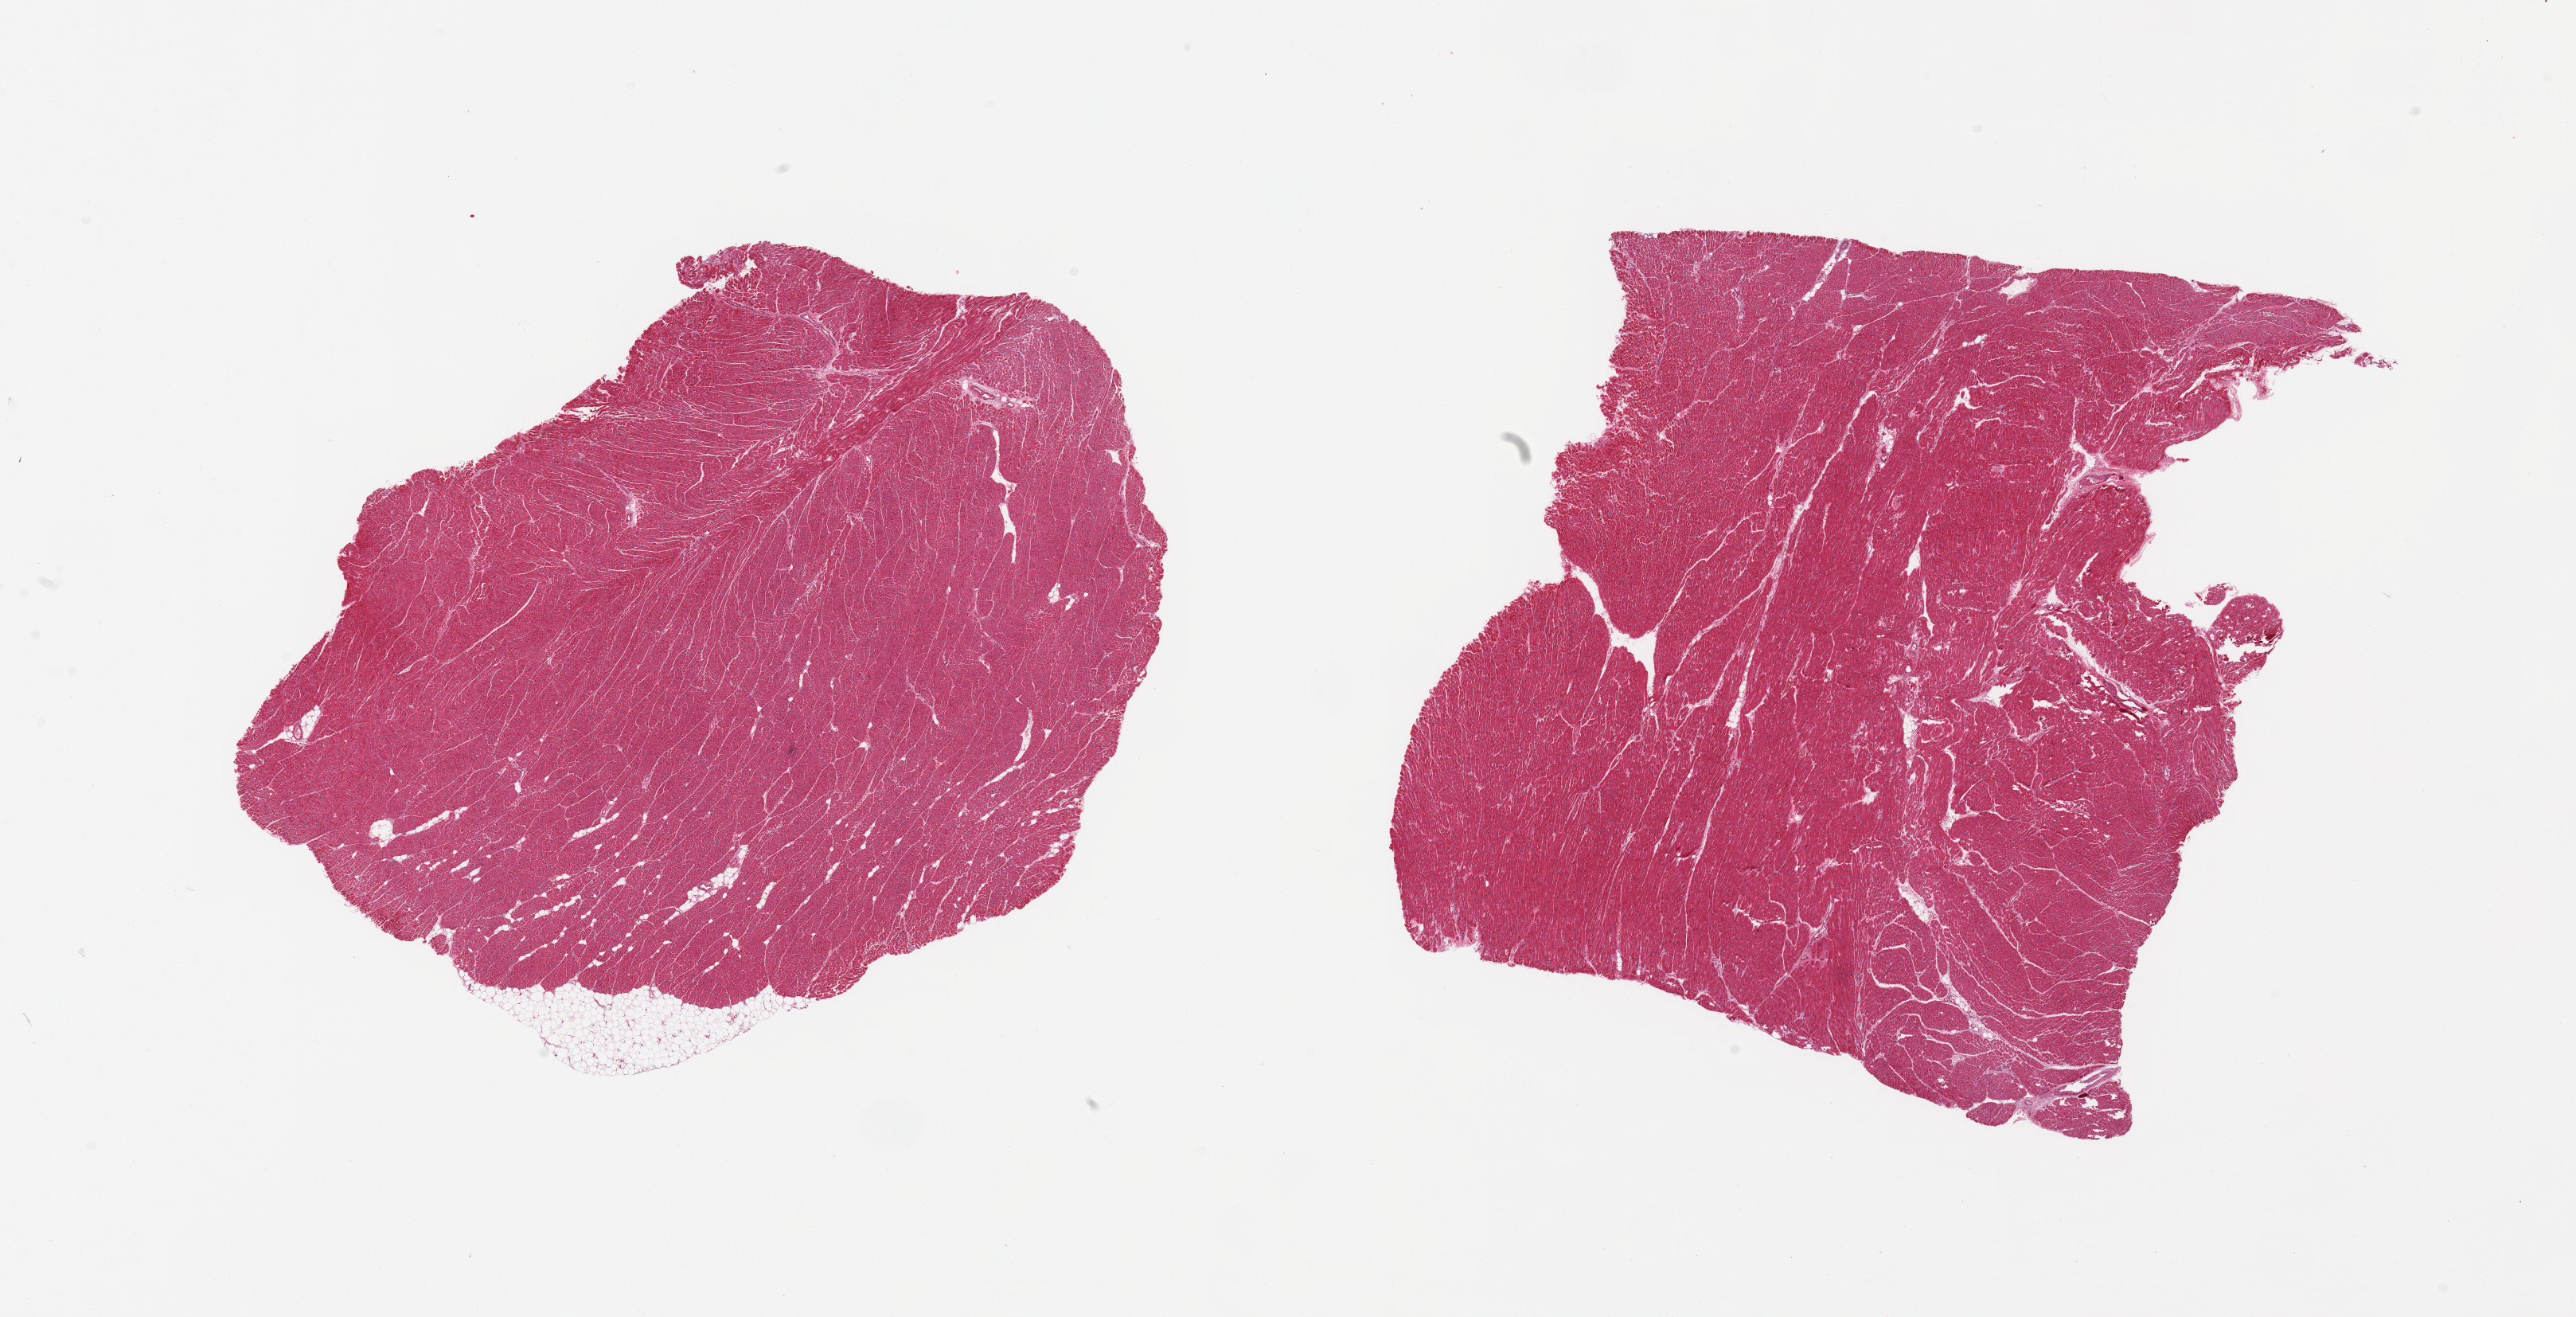
H&E whole-slide image, brightfield, shown as a low-resolution overview of the whole scanned area (about 25.6 x 13.1 mm). PAXgene-fixed, paraffin-embedded tissue. Section of heart (target tissue). Donor tissue sample. Male donor.
• pathologist's review note for this sample: 2 pieces, moderate interstitial fibrosis/chronic ischemic changes